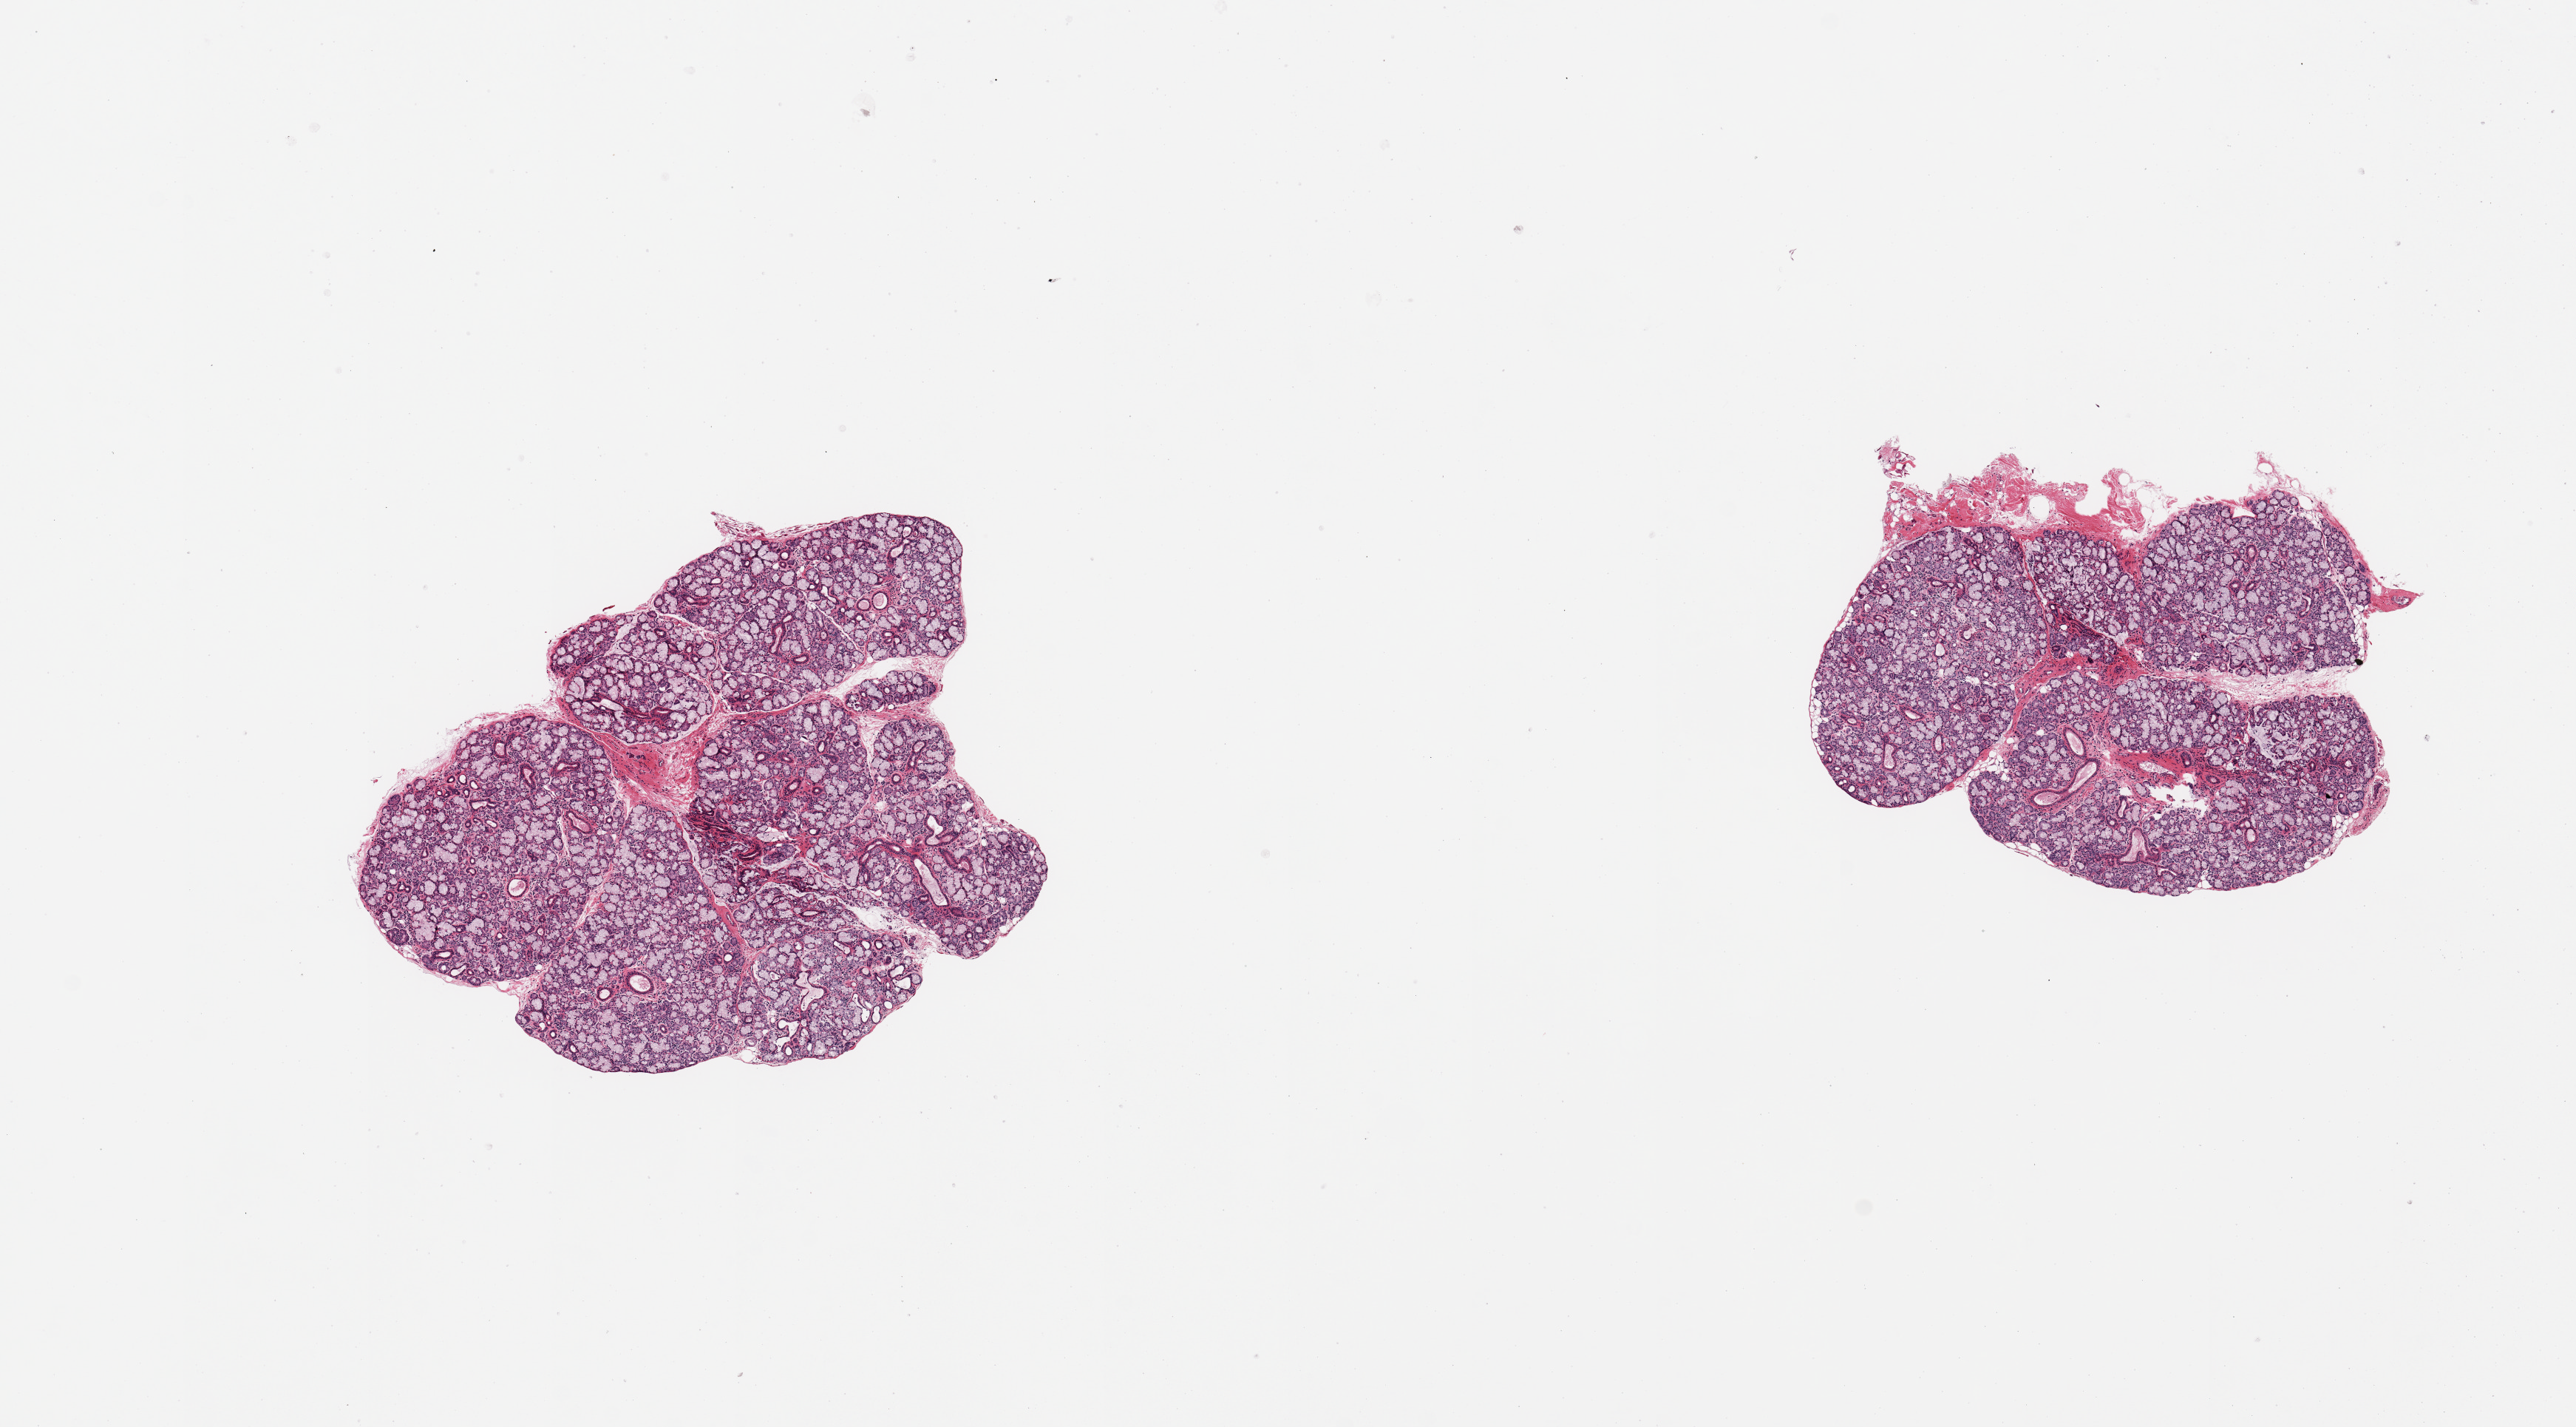
Haematoxylin and eosin whole-slide image, shown as a low-resolution overview of the whole scanned area (about 13.8 x 7.6 mm, acquisition: 20x scan). PAXgene-fixed, paraffin-embedded tissue. Target tissue: minor salivary gland. Donor tissue sample. Donor: male.
Review note (as recorded): 2 pieces; well dissected.